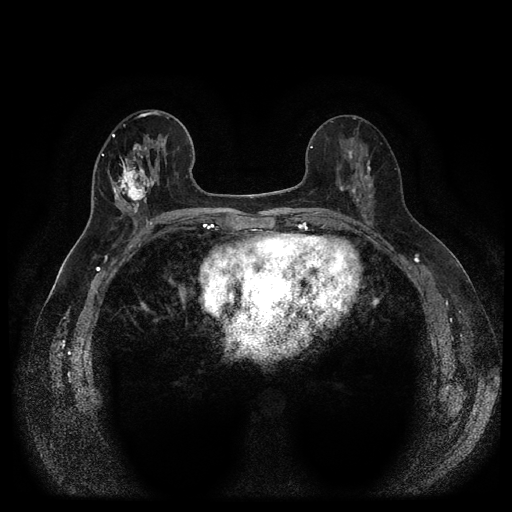
Breast MRI (dynamic contrast-enhanced, multi-phase), one axial slice. Slice 44 of 116 in the series (ordered by position). Dynamic contrast-enhanced series, time point 2 of 5 at this slice position (early post-contrast). 1.5 T. TE 2.6 ms, TR 5.4 ms. 2 mm slice thickness. 512 × 512 image matrix, field of view 340 × 340 mm. Patient: female, 56 years.
Structures marked on this image (semi-automatic segmentation, software-assisted and operator-edited):
- breast lesion (labelled 'tumour' in the annotation; benign lesions carry a separate 'benign' label): bounding box (x1, y1, x2, y2) in pixels: (107, 154, 160, 216)